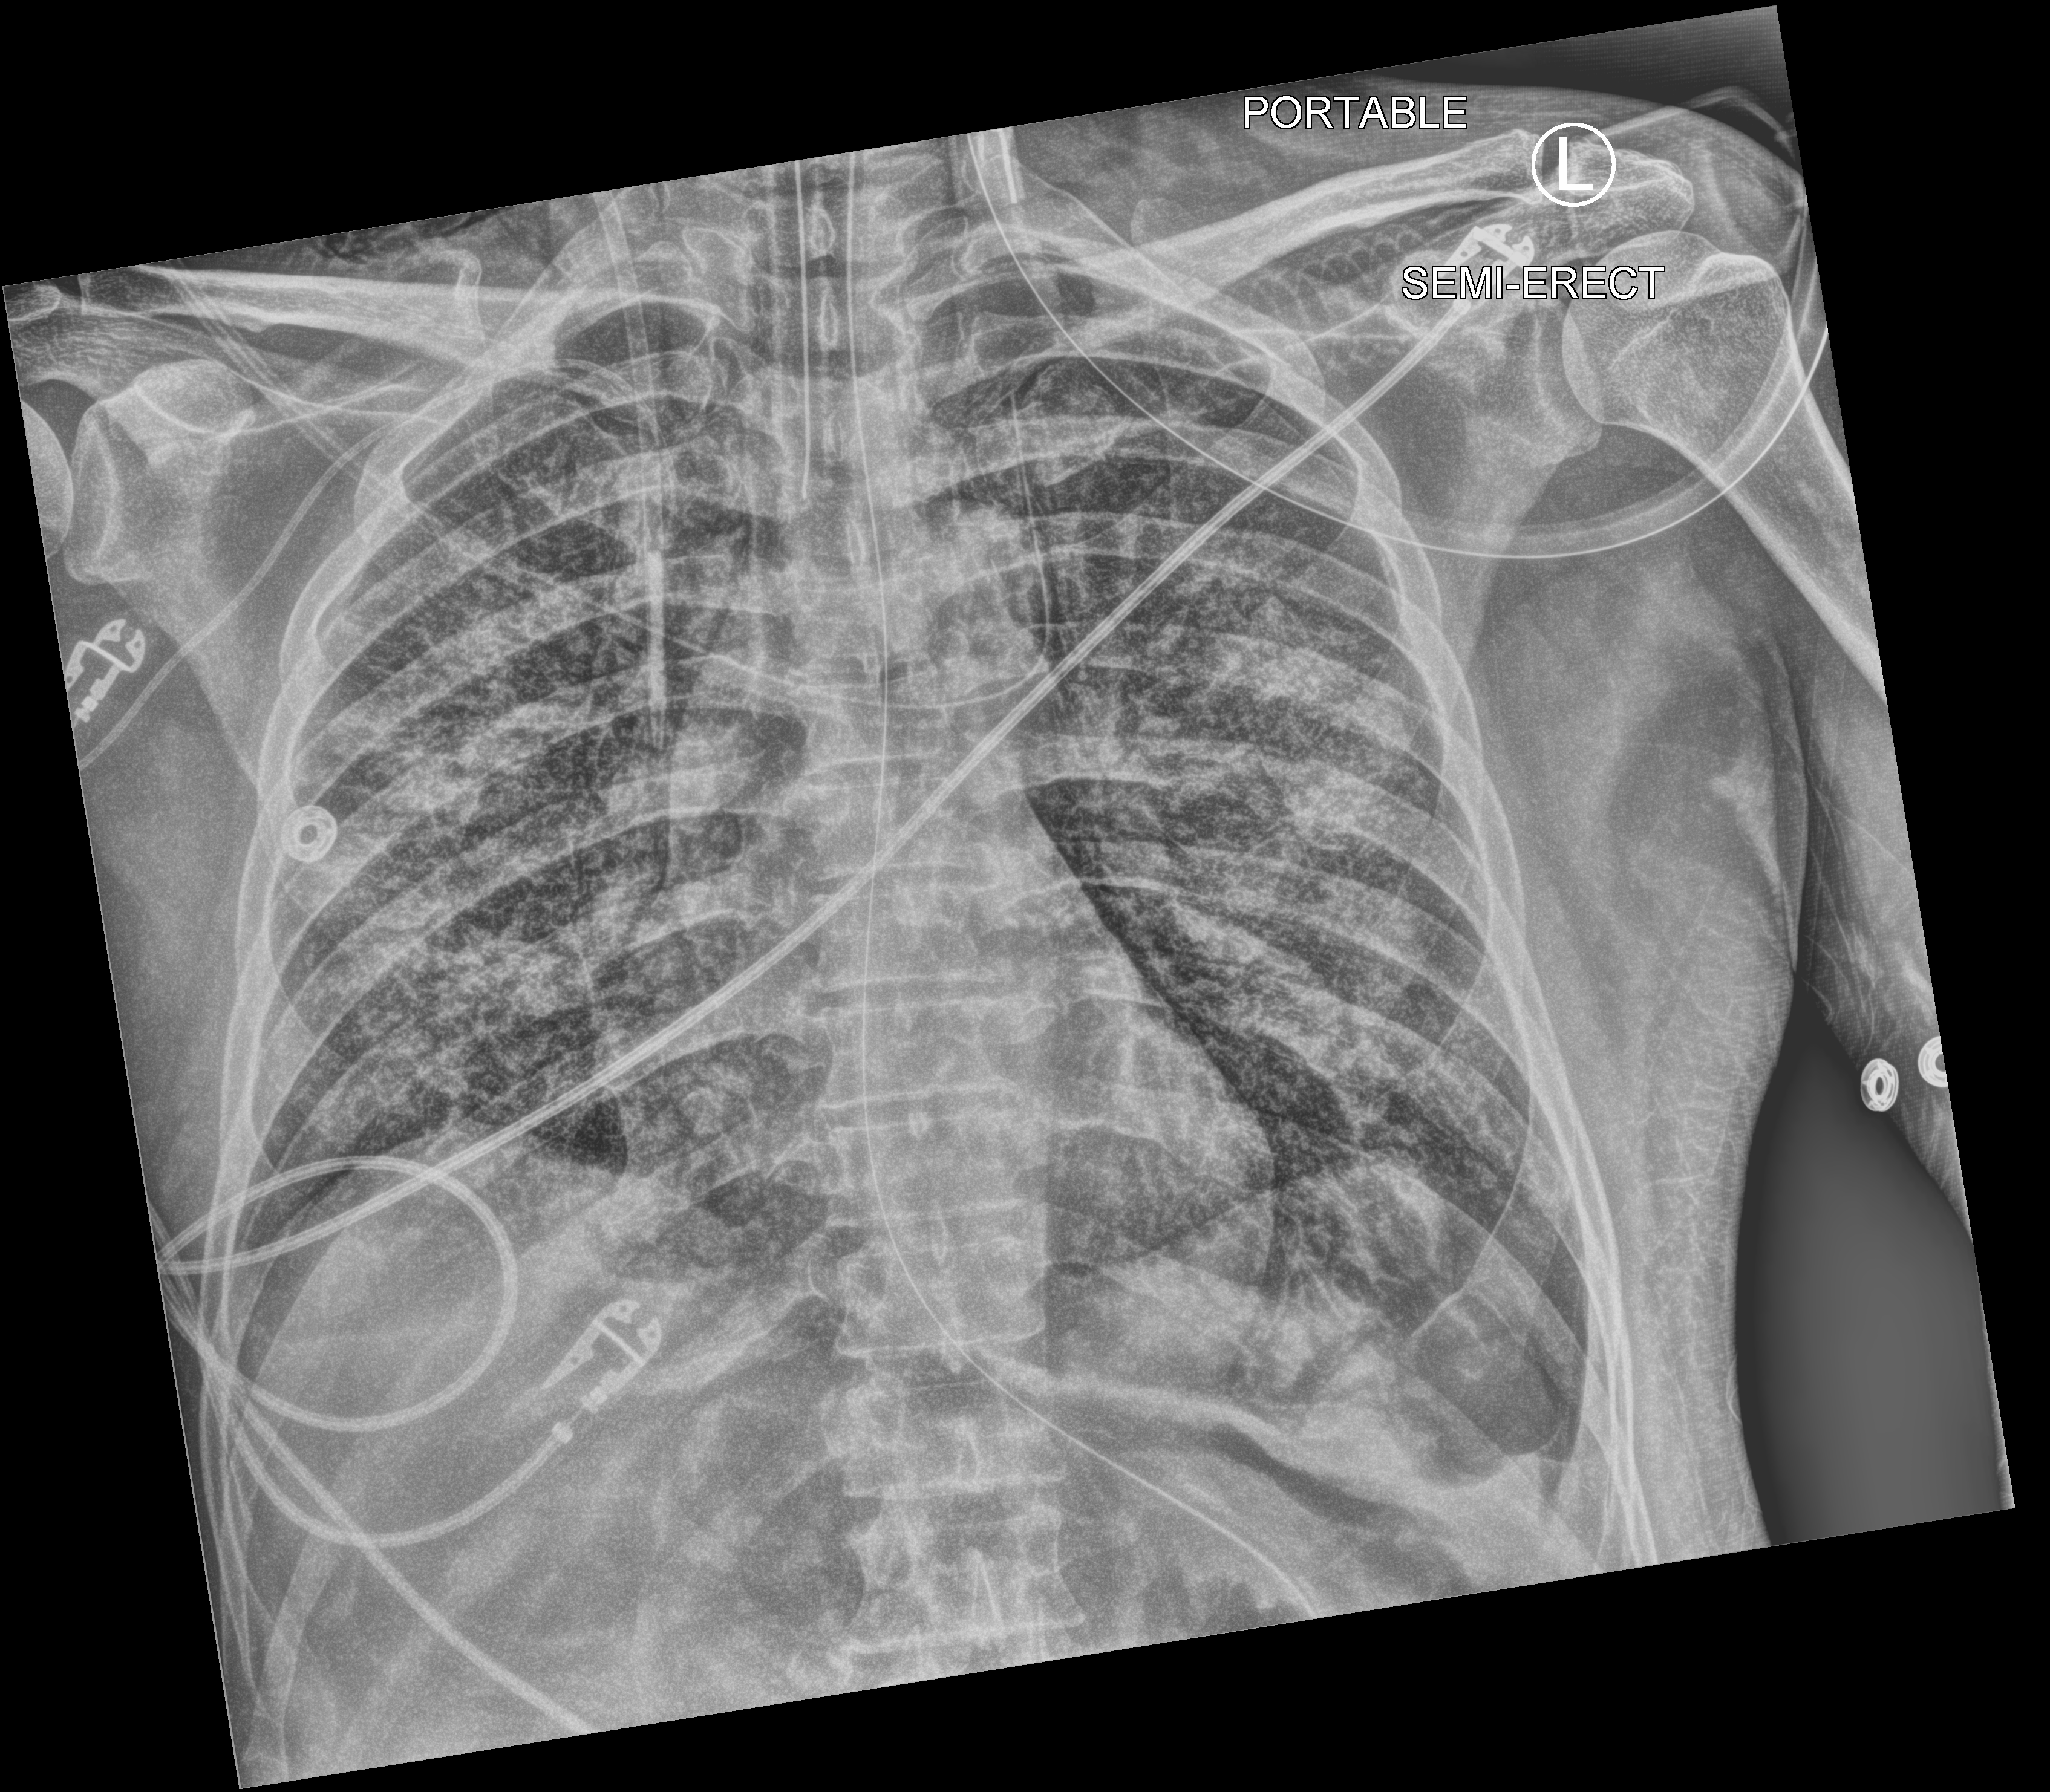
Chest X-ray (portable). Patient hospitalised with COVID-19; male, aged 18–59 years.
From the hospital-stay record, not from the radiograph (when in the stay this image was taken is not recorded): other chronic lung disease (admission record): no; length of hospital stay: 77 days; mechanically ventilated during this hospital stay: yes.